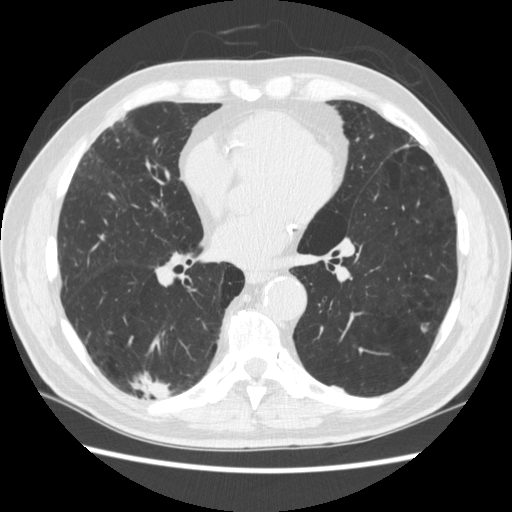
Low-dose screening chest CT, one axial slice. Position 121 of 266 along the scan axis. Reconstruction kernel STANDARD. Lung window (W 1500 / L -600 HU). 1.25 mm slice thickness. 512 × 512 image matrix.
Structures marked on this image (outlined manually by an expert reader):
- lesion 1 (tumor, upper lobe of right lung): bounding box [x1, y1, x2, y2] px = [138, 375, 170, 399]